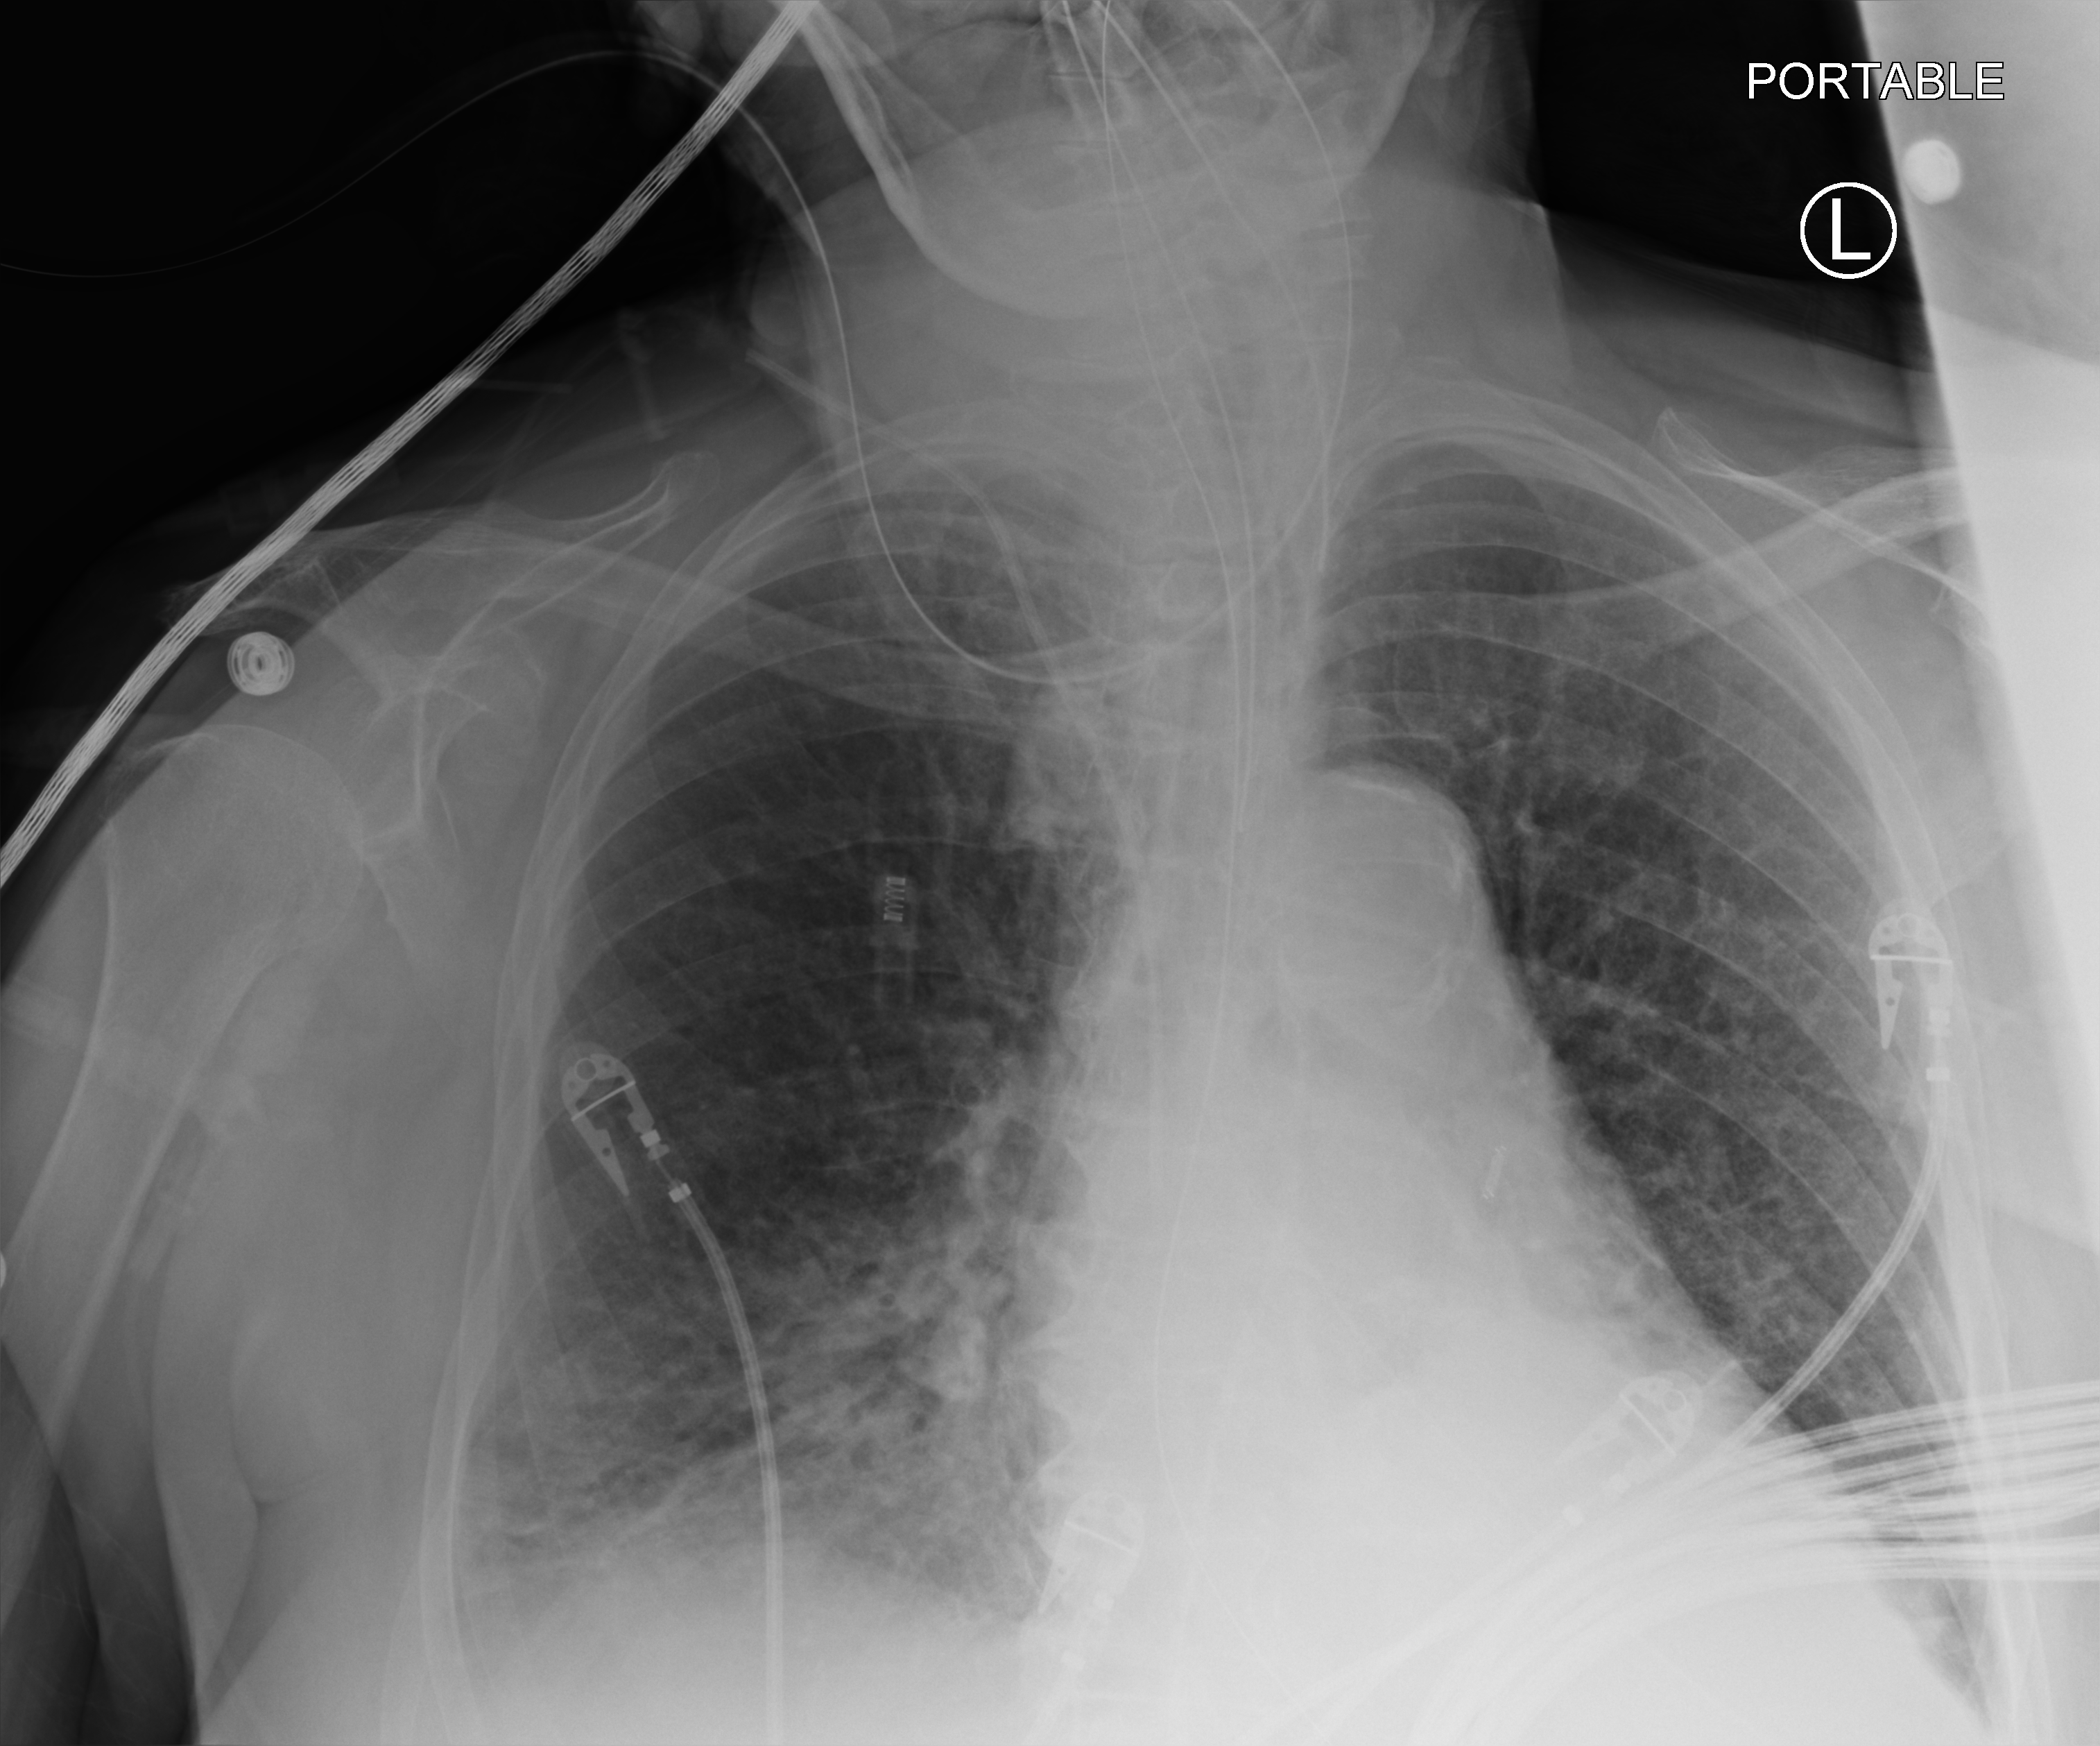
Bedside chest radiograph (computed radiography). Patient hospitalised with COVID-19; female, aged 75–90 years.
From the hospital-stay record, not from the radiograph (when in the stay this image was taken is not recorded): smoking status (admission record): former; admitted to intensive care during this hospital stay: yes.